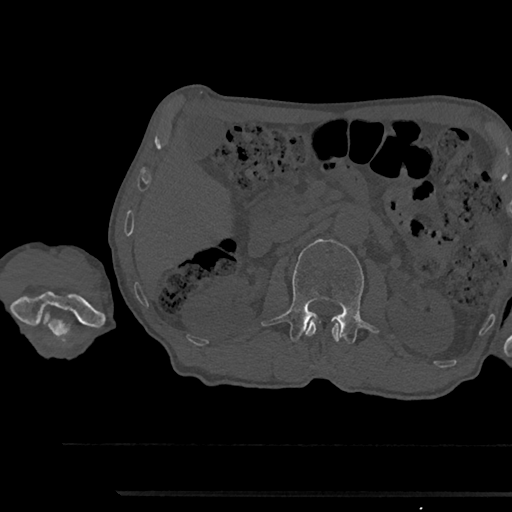
CT including the spine, one axial slice. Slice 587 of 797 in the series (ordered by position). Reconstruction kernel Br40s/3. Bone window (W 1800 / L 400 HU). 0.5 mm slice thickness. 512 × 512 image matrix. Male patient, age 79 years. From the clinical record (not read from this slice): primary cancer: prostate.
Annotated regions visible in this slice (semi-automatic segmentation, software-assisted and operator-edited):
- L1 vertebra: bounding box <305,319,341,342> (left, top, right, bottom; pixels)
- L2 vertebra: <261,239,378,343>